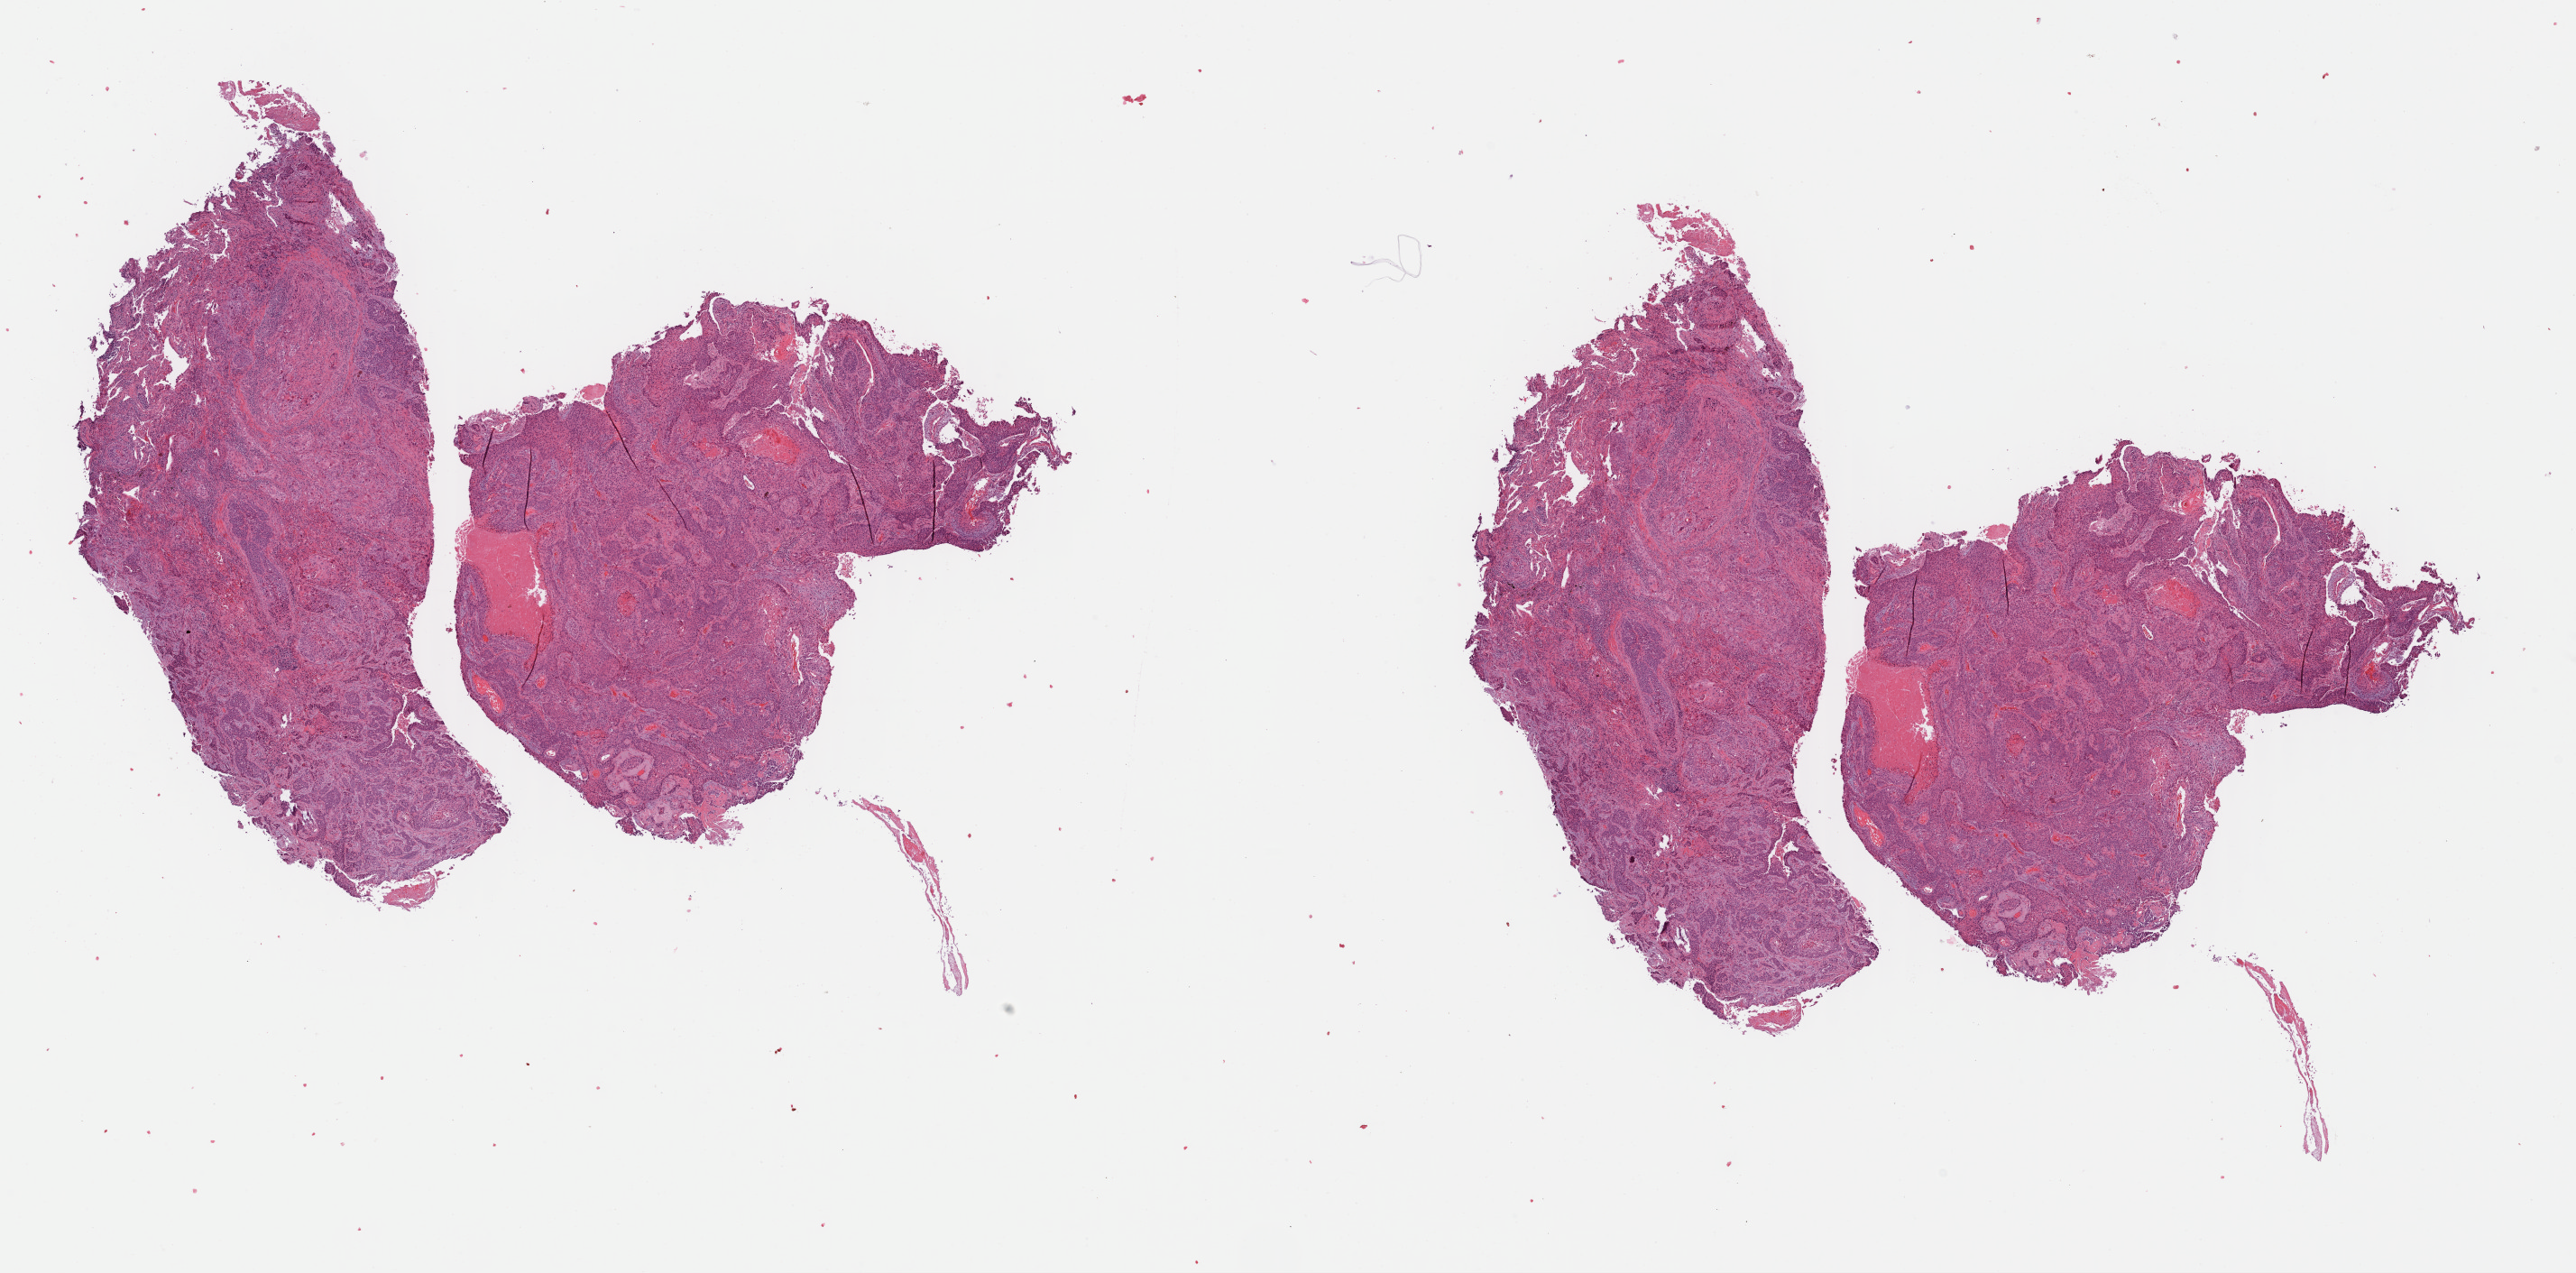
Whole-slide histology image, H&E — low-resolution overview of the scanned area, about 22.4 x 11.1 mm, formalin-fixed paraffin-embedded (FFPE) diagnostic section, sample: primary tumour, lung. Patient: male, age at initial diagnosis 63 years.
AJCC pathologic stage: IIB (7th edition). Histologic diagnosis: Squamous cell carcinoma, NOS.